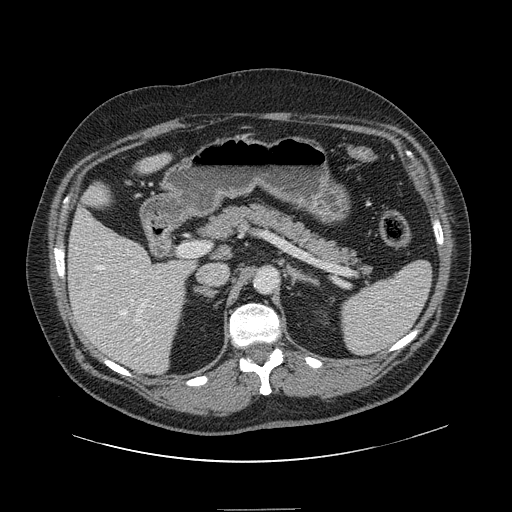
Contrast-enhanced abdominal CT, one axial slice; slice 77 of 154 in the series (ordered by position); 120 kVp; intravenous contrast given; soft-tissue window (W 400 / L 40 HU); 2.5 mm slice thickness; 512 × 512 image matrix. Male patient, age 61 years. From the clinical record (not read from this slice): diagnosis: colorectal cancer liver metastases, imaged before liver resection.
Outlined on this slice (expert manual segmentation):
- hepatic veins: bounding box <96,265,140,341> (left, top, right, bottom; pixels)
- liver: <68,158,194,373>
- planned liver remnant (the part of the liver to remain after resection): <69,158,194,365>
- portal vein (with intrahepatic branches): <132,270,149,323>
- liver metastasis: <78,281,82,287>